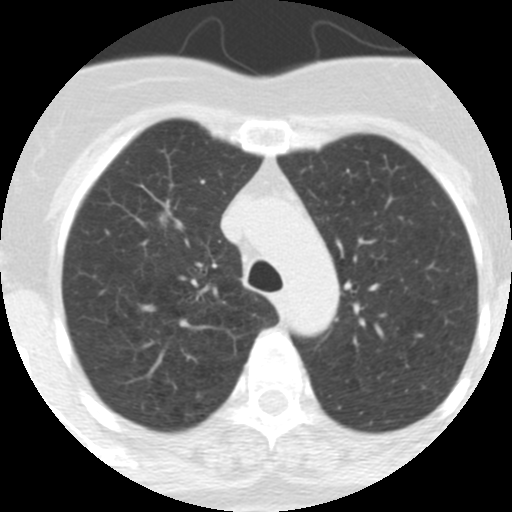
Low-dose screening chest CT, one axial slice; position 236 of 313 along the scan axis; reconstruction kernel STANDARD; 120 kVp; lung window (W 1500 / L -600 HU); 512 × 512 image matrix, field of view 253 × 253 mm.
Annotated regions visible in this slice (manually delineated by an expert):
- lesion 1 (tumor, upper lobe of right lung): bounding box (x1, y1, x2, y2) in pixels: (160, 214, 168, 222)